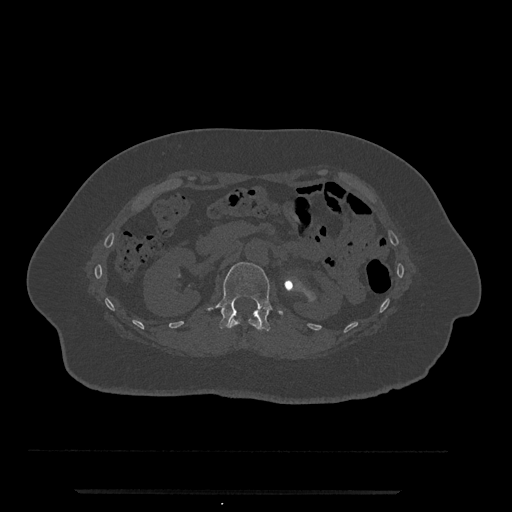
CT including the spine, one axial slice; position 119 of 797 along the scan axis; 120 kVp; bone window (W 1800 / L 400 HU); 512 × 512 image matrix, field of view 440 × 440 mm. Patient: female, 51 years. From the clinical record (not read from this slice): primary cancer: neuro.
Annotated regions visible in this slice (semi-automatic segmentation, software-assisted and operator-edited):
- L1 vertebra: bounding box (x1, y1, x2, y2) in pixels: (208, 262, 283, 331)
- T12 vertebra: (228, 317, 262, 331)